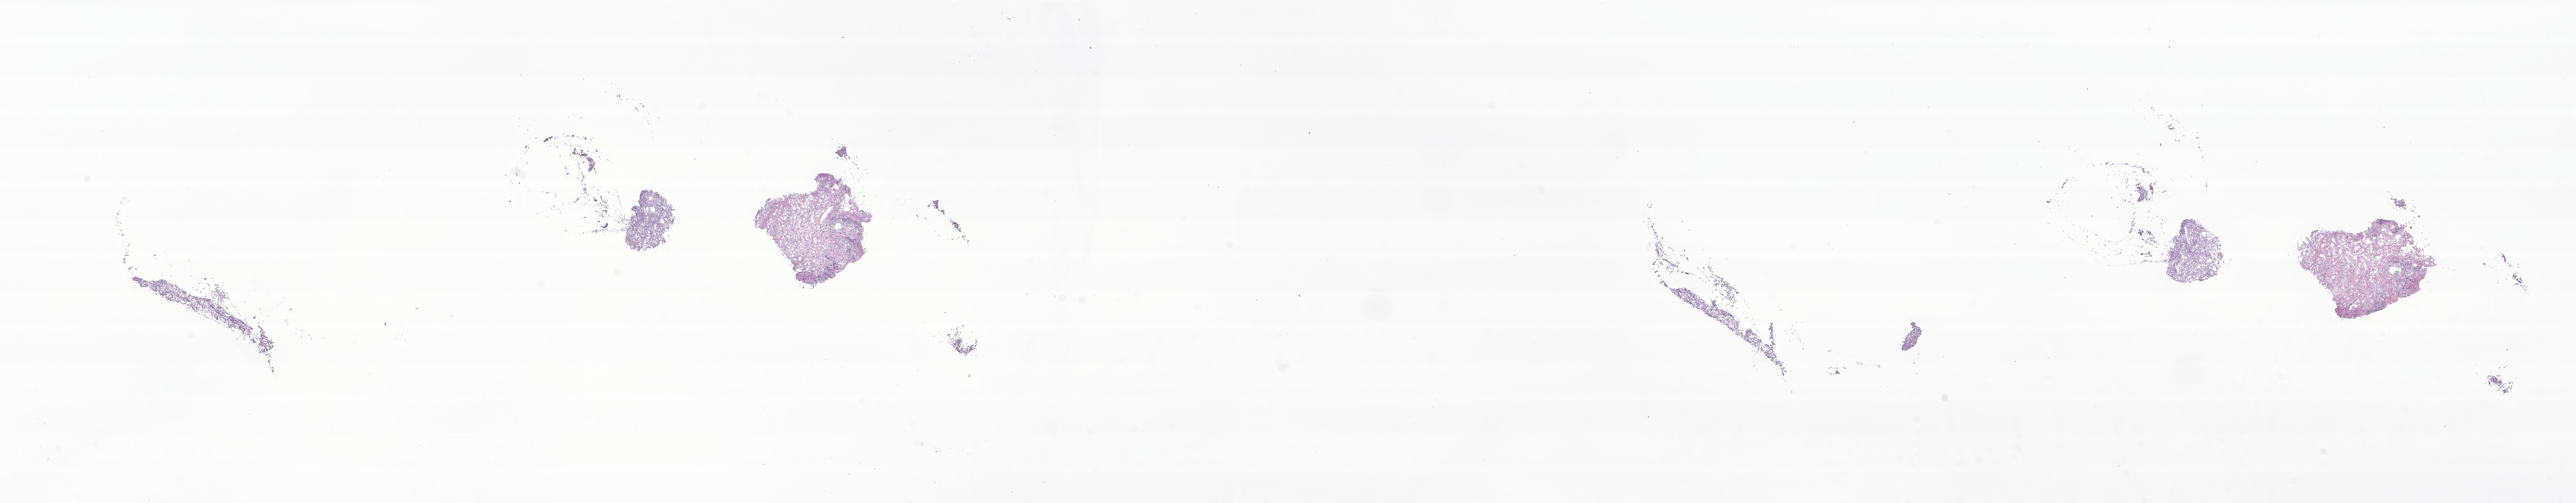
Whole-slide image, hematoxylin and eosin (H&E) stain of tumor tissue from the soft tissue of thorax, low-resolution overview of the scanned area, about 38.5 x 7.5 mm. Cryosection (OCT / tissue freezing medium). Patient: female, age 104 months.
Diagnosis (ICD-O-3 morphology term): Sarcoma, NOS.